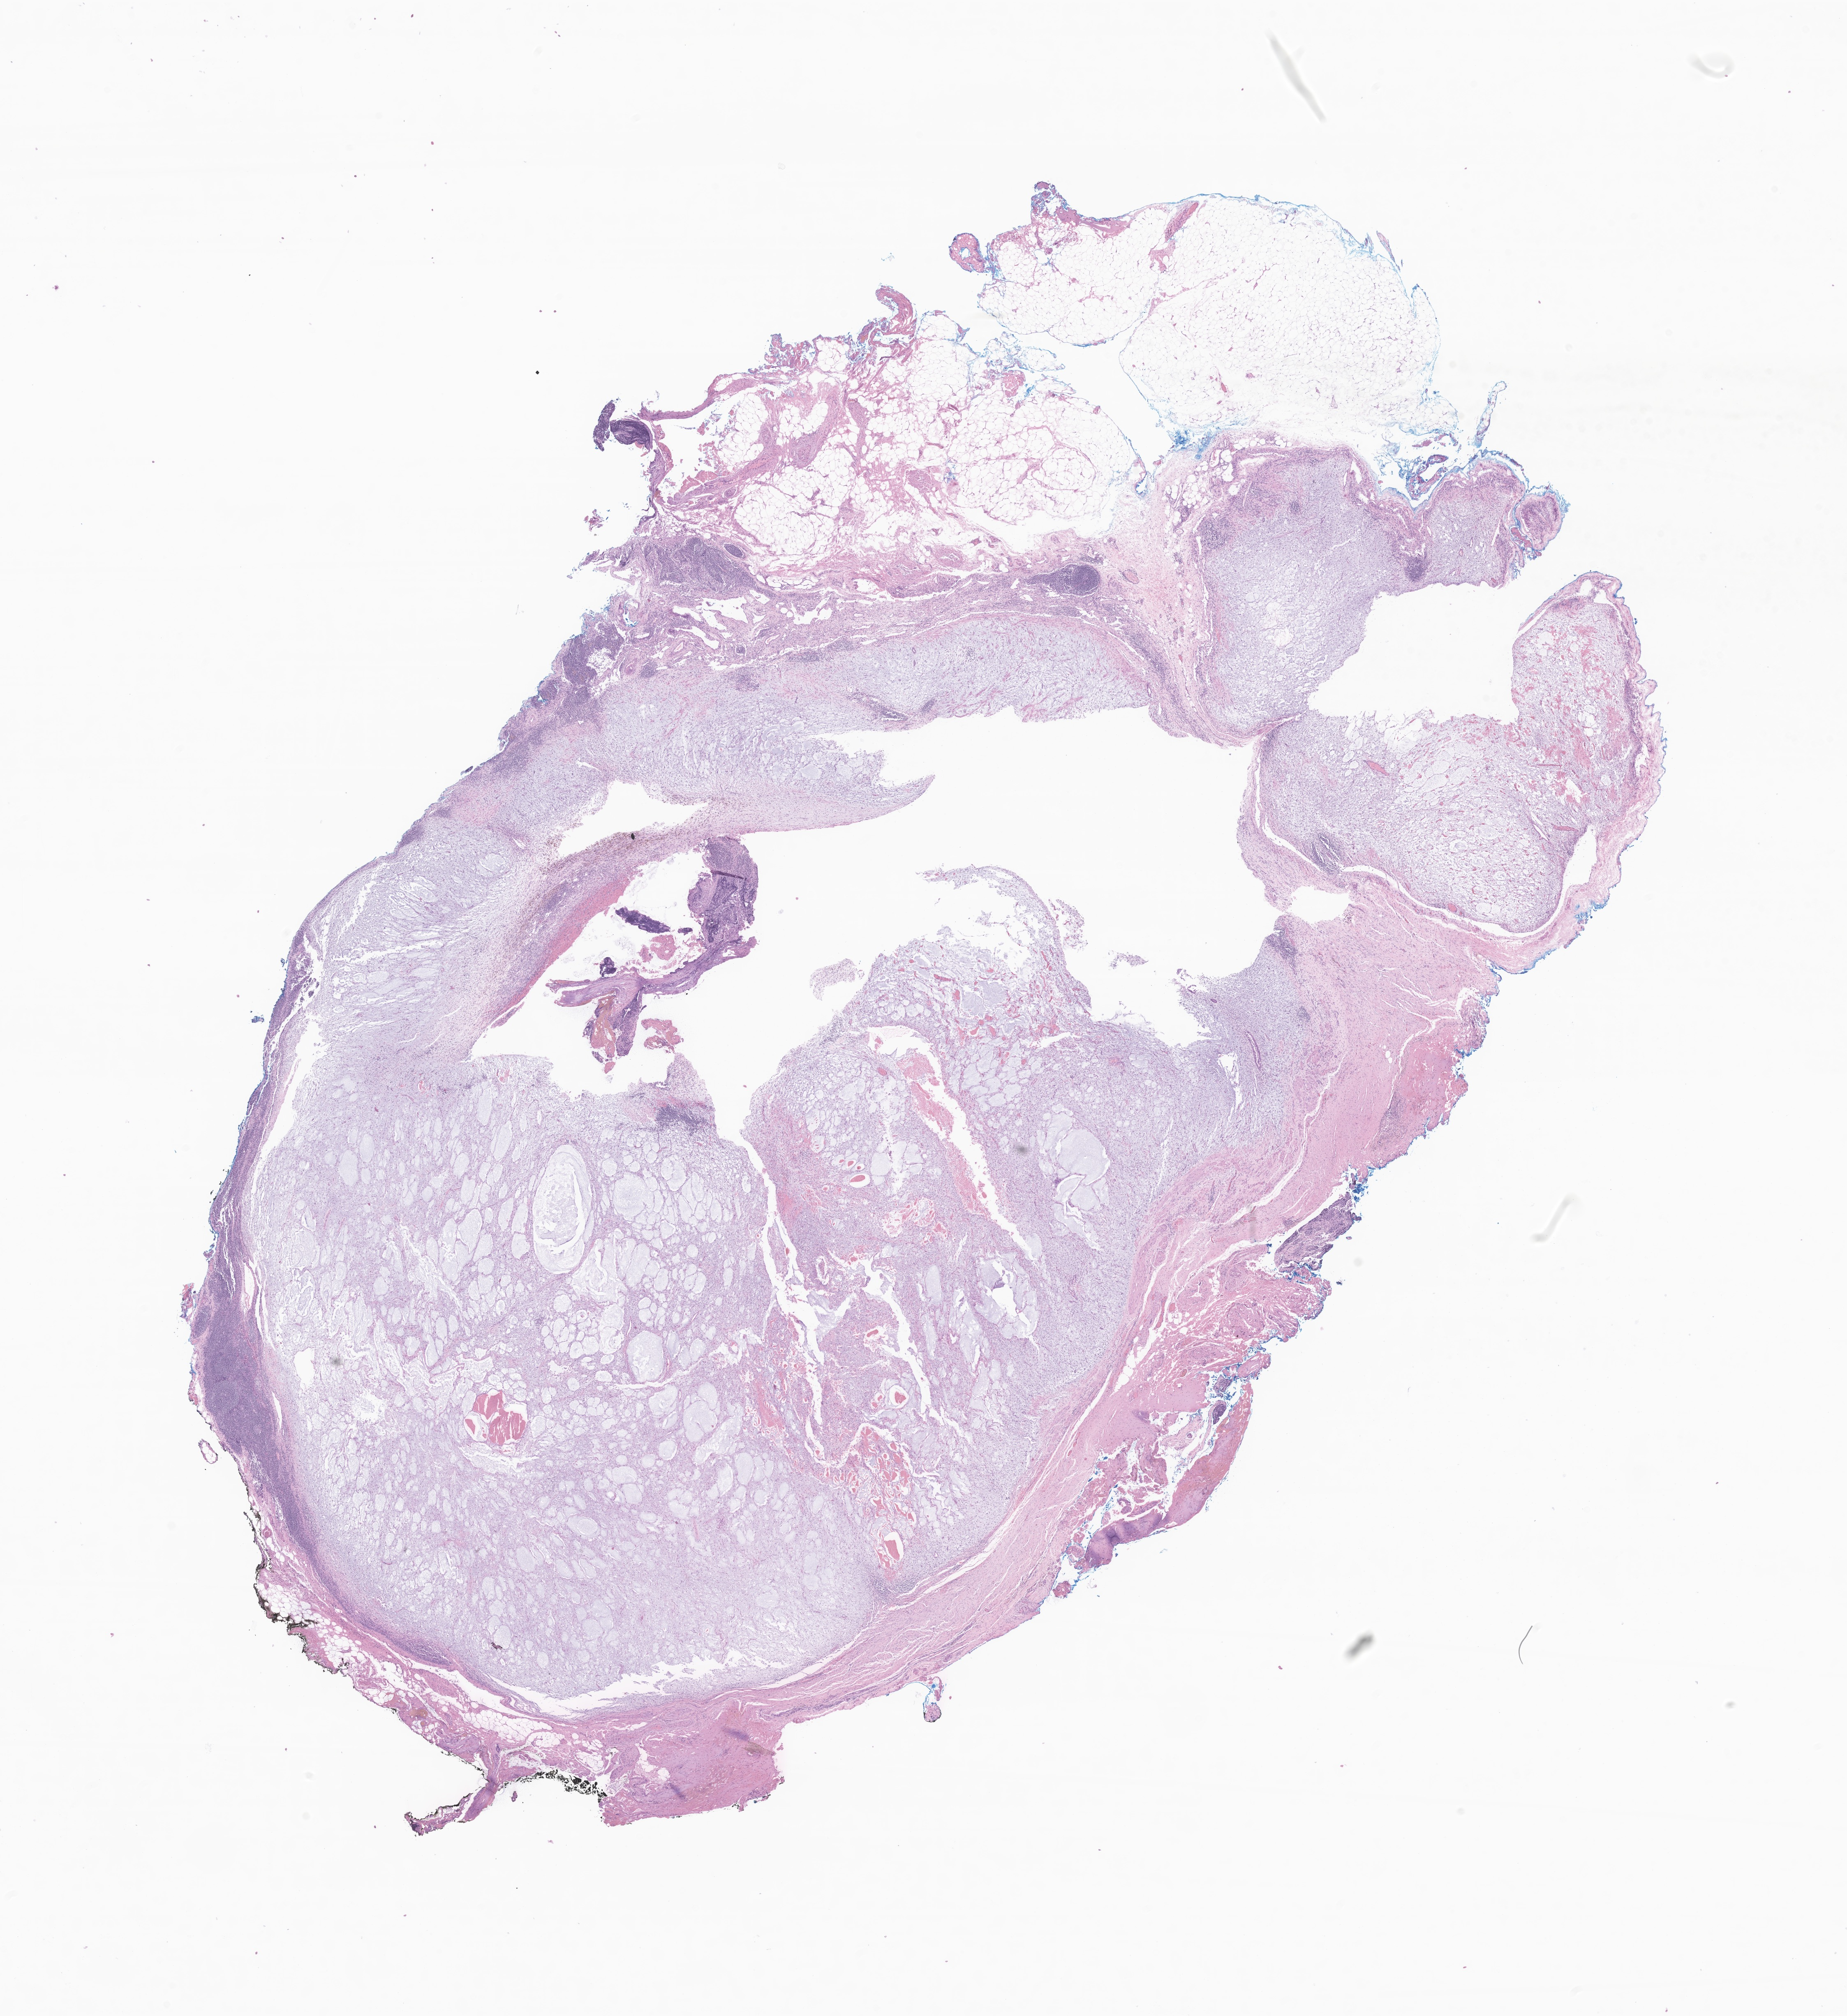
Digitized H&E-stained section of tumor tissue from the abdomen — low-resolution overview of the scanned area, about 18.9 x 20.7 mm; formalin-fixed, paraffin-embedded (FFPE) tissue. Patient female; age 133 months (11 years 1 month).
Diagnosis: Sarcoma, NOS.